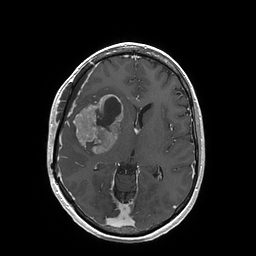
Brain MRI from a brain-tumour surgery series, one axial slice; position 88 of 202 along the scan axis; T1-weighted post-contrast; 1 mm slice thickness; 256 × 256 image matrix. From the clinical record (not read from this slice): histopathology: Glioblastoma; WHO grade: 4; IDH mutation: no.
Structures marked on this image (outlined manually by an expert reader):
- tumour: bounding box (x1, y1, x2, y2) in pixels: (73, 94, 123, 154)